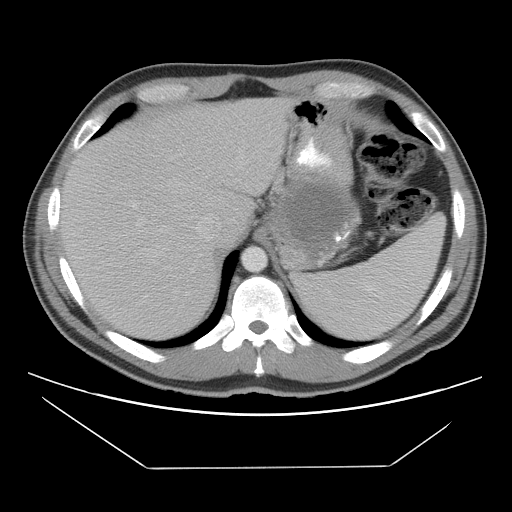
Contrast-enhanced abdominal CT, one axial slice; slice 81 of 131 in the series (ordered by position); reconstruction kernel STANDARD; soft-tissue window (W 400 / L 40 HU); 5 mm slice thickness; 512 × 512 image matrix, field of view 396 × 396 mm. Patient: male, 44 years. Case-level facts recorded for this patient, not image findings: diagnosis: adrenocortical carcinoma; tumour side: left adrenal; tumour size at pathology: 15.5 cm.
Outlined on this slice (semi-automatically segmented with operator editing):
- mass: bounding box [x1, y1, x2, y2] px = [286, 184, 341, 243]